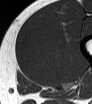
MRI of an extremity soft-tissue mass, one axial slice; position 24 of 62 along the scan axis; MR volume resampled by the dataset authors to the PET/CT grid (not the native acquisition matrix); 92 × 104 image matrix, field of view 90 × 102 mm. Male patient. Case-level facts recorded for this patient, not image findings: histological type: mixoid liposarcoma; grade: low; site of the primary tumour: left thigh.
Outlined on this slice (expert contour drawn on MRI and transferred to this co-registered scan by the dataset authors):
- gross tumour volume (mass): bounding box <19,22,67,84> (left, top, right, bottom; pixels)